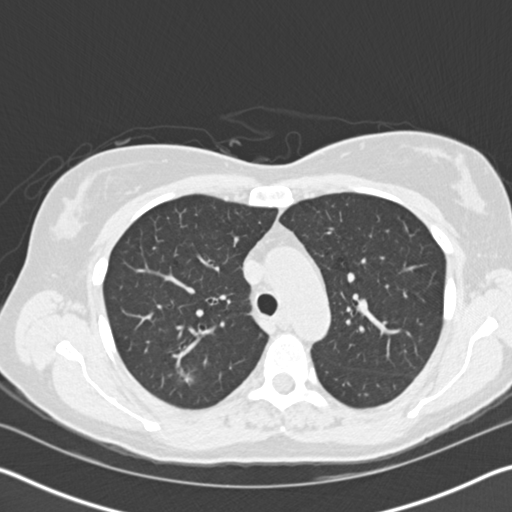
Low-dose screening chest CT, axial slice. First (baseline) screen. Lung window (W 1500 / L -600 HU). Female, age 58 years at enrolment.
Lesion marked by an expert reader, bounding box <160,351,217,405> (left, top, right, bottom; pixels). The screening reader recorded 3 non-calcified nodules or masses ≥4 mm on this exam; which of them this box marks is not recorded. Later outcome: lung cancer diagnosed 487 days after this screen — bronchiolo-alveolar adenocarcinoma, NOS, right upper lobe, moderately differentiated (G2), stage IA (AJCC 6th edition), 7 mm at pathology.